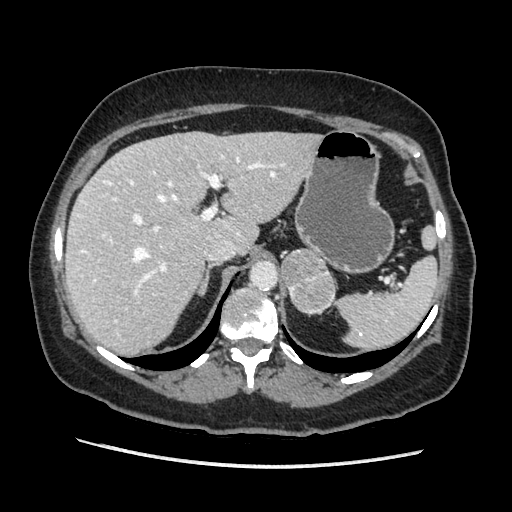
Contrast-enhanced abdominal CT, one axial slice. Soft-tissue window (W 400 / L 40 HU). 512 × 512 image matrix, field of view 360 × 360 mm. Female patient. Case-level facts recorded for this patient, not image findings: diagnosis: adrenocortical carcinoma; tumour side: left adrenal.
Structures marked on this image (semi-automatically segmented with operator editing):
- mass: bounding box (x1, y1, x2, y2) in pixels: (282, 249, 335, 312)